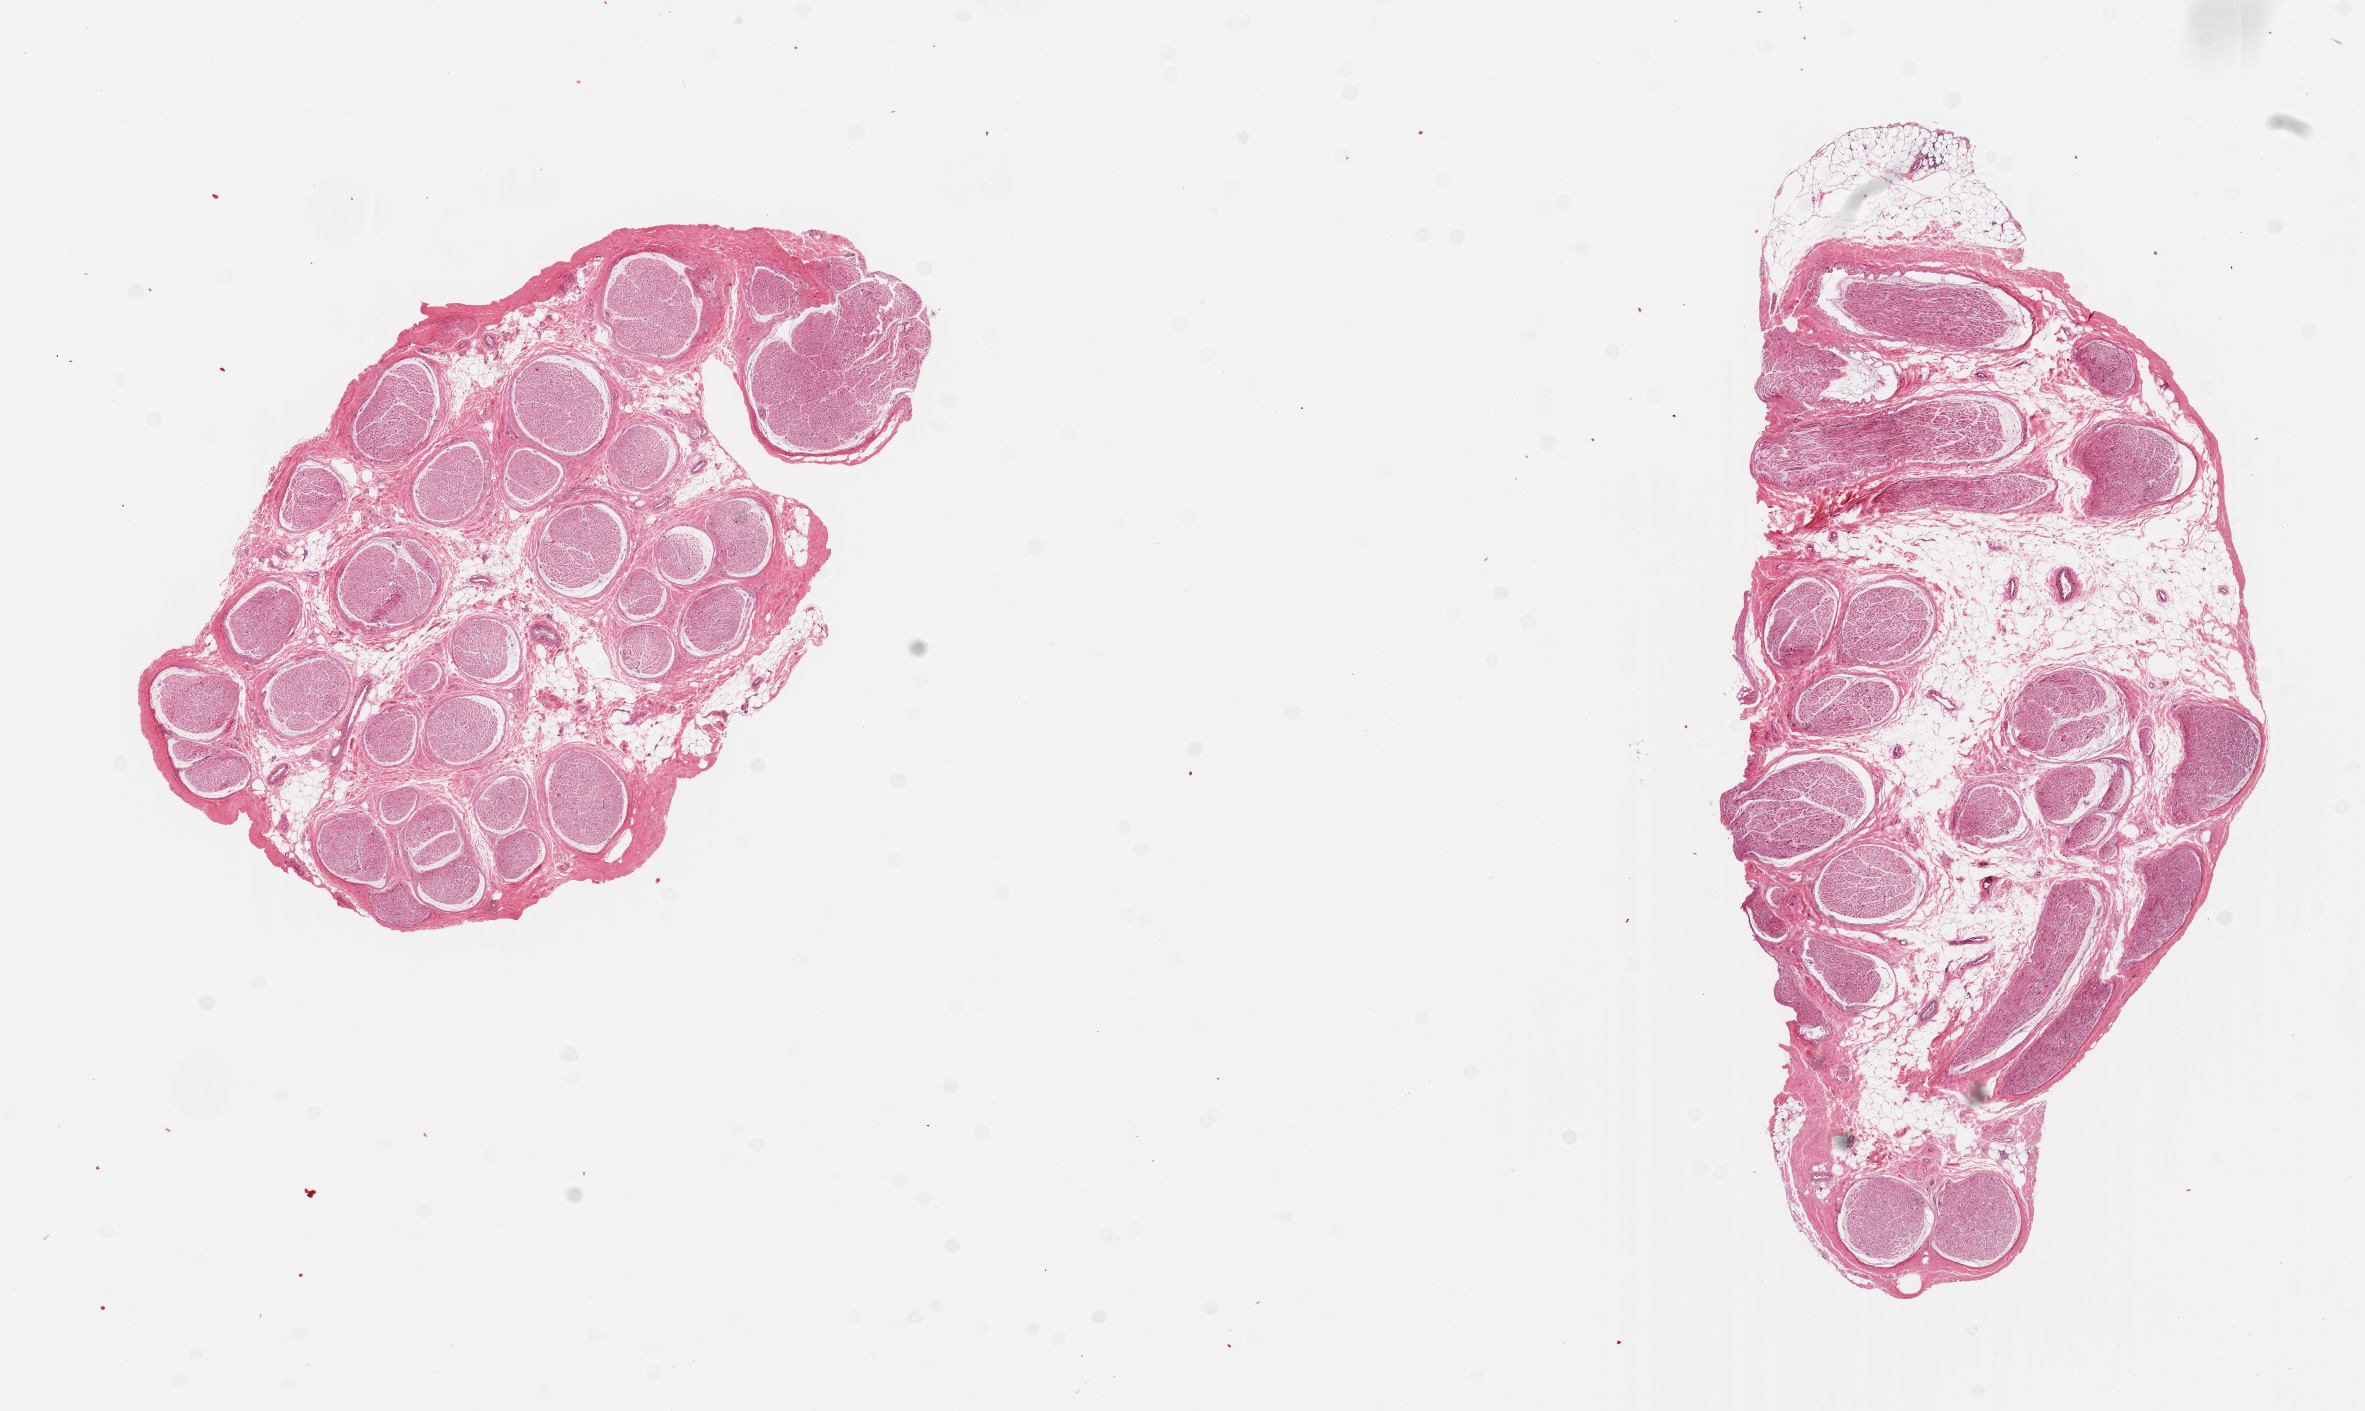
Whole-slide image, haematoxylin and eosin stain — a low-resolution overview of the entire scanned area, about 18.7 x 11.2 mm; PAXgene-fixed paraffin-embedded (PFPE) section; section of tibial nerve (target tissue); donor tissue sample. Donor sex: female.
- review note (as recorded): 2 pieces; 20 & 40% internal fat